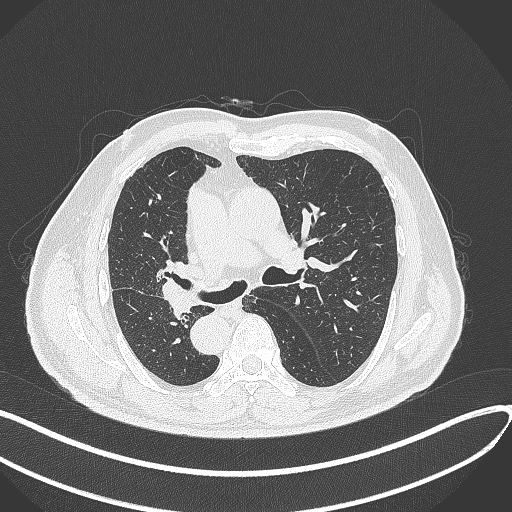
Chest CT, one axial slice. Lung window (W 1500 / L -600 HU). 1 mm slice thickness. 512 × 512 image matrix, field of view 400 × 400 mm. Patient: male, 67 years. Case-level facts recorded for this patient, not image findings: clinical TNM (as recorded): T2a N0 M0.
Annotated regions visible in this slice (bounding box drawn by a radiologist):
- lung tumour (recorded histology: squamous cell carcinoma): bounding box <156,271,202,319> (left, top, right, bottom; pixels)